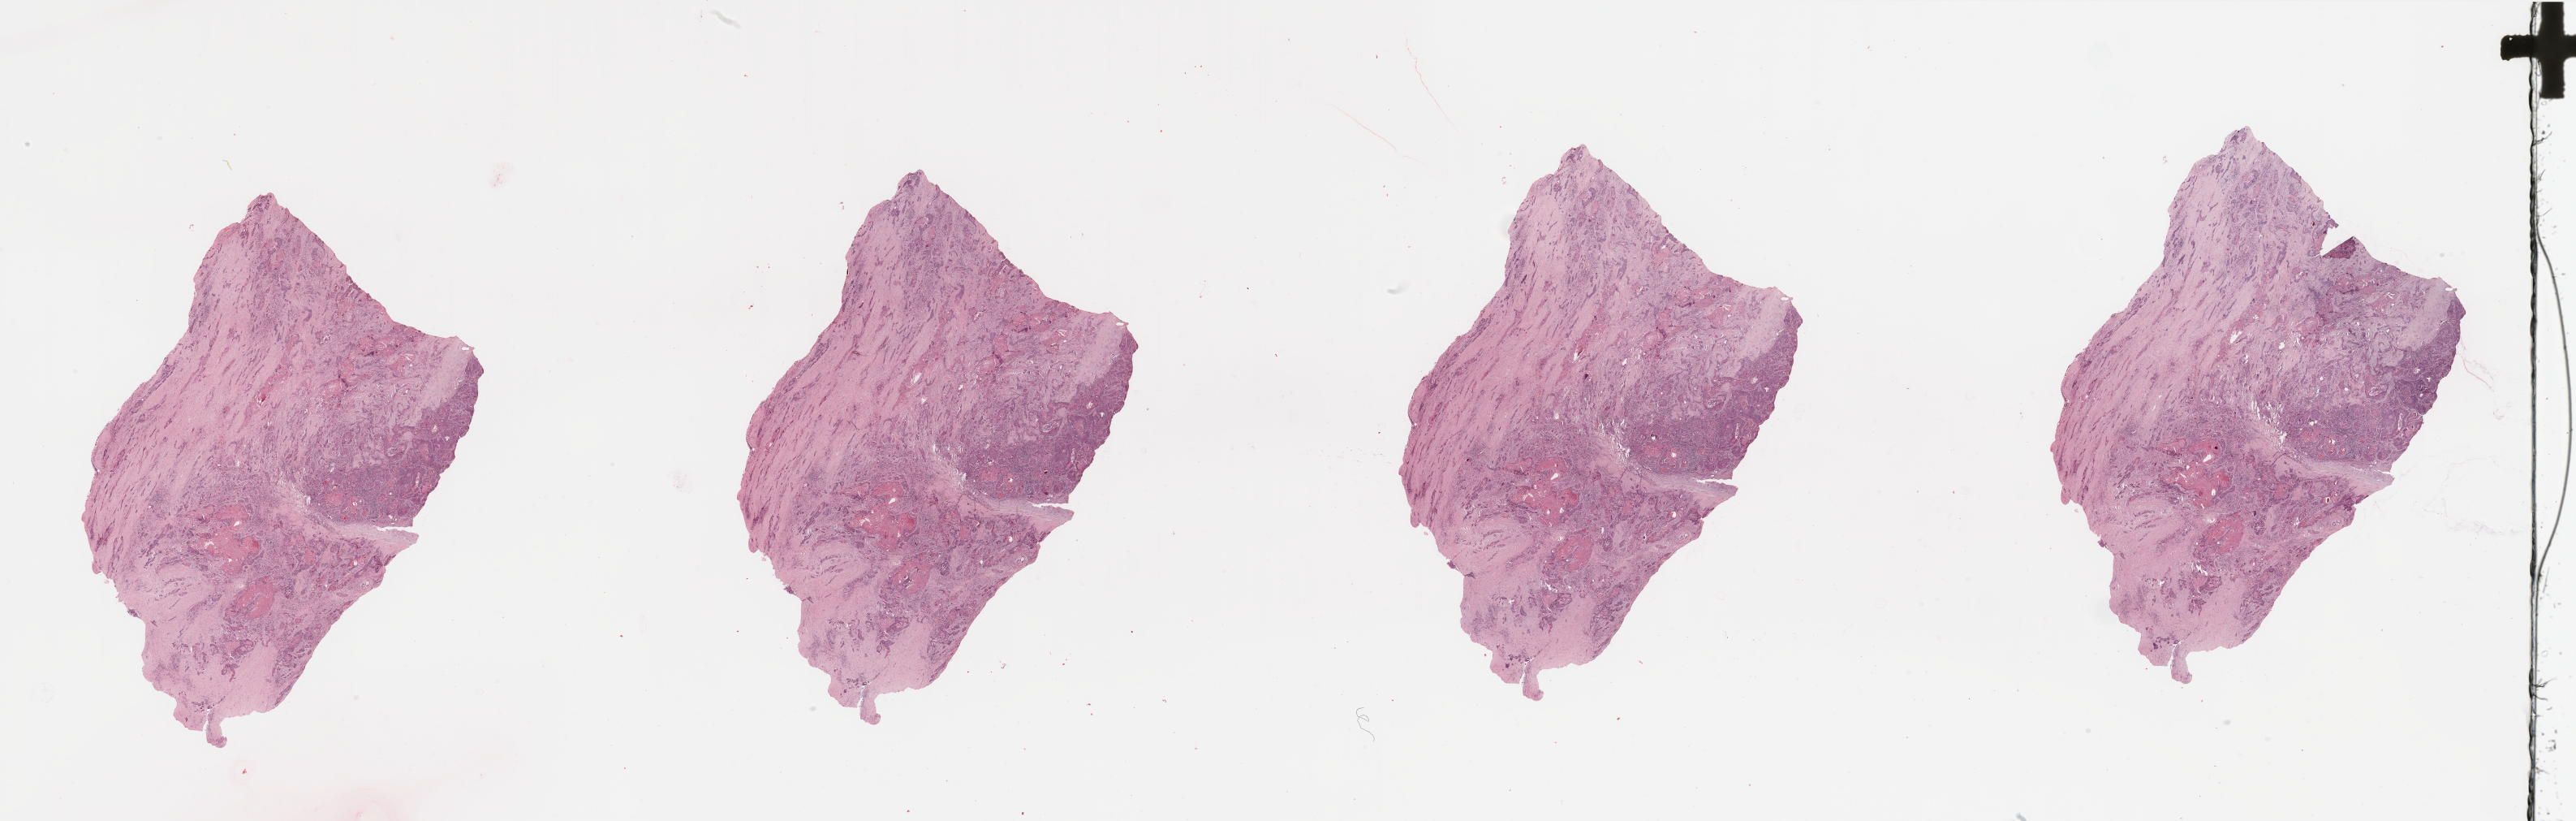
H&E-stained whole-slide image — shown as a low-resolution overview of the whole scanned area (about 50.2 x 16.0 mm, from a 20x scan); head and neck, tissue type not recorded. 81-year-old male patient.
Patient diagnosis: Squamous cell carcinoma, NOS (larynx, NOS).